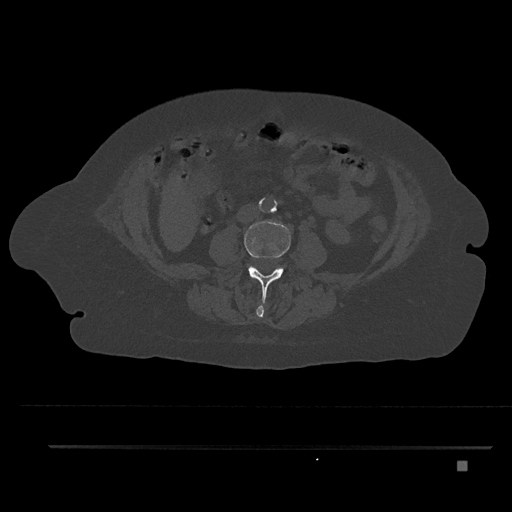
CT including the spine, one axial slice. Slice 123 of 797 in the series (ordered by position). Reconstruction kernel Br40s/3. Bone window (W 1800 / L 400 HU). 0.5 mm slice thickness. 512 × 512 image matrix, field of view 437 × 437 mm. Patient: female, 76 years. From the clinical record (not read from this slice): primary cancer: lung.
Structures marked on this image (semi-automatically segmented with operator editing):
- L2 vertebra: box from (x=256, y=305) to (x=264, y=318) px
- L3 vertebra: (x=244, y=220)–(x=291, y=306)